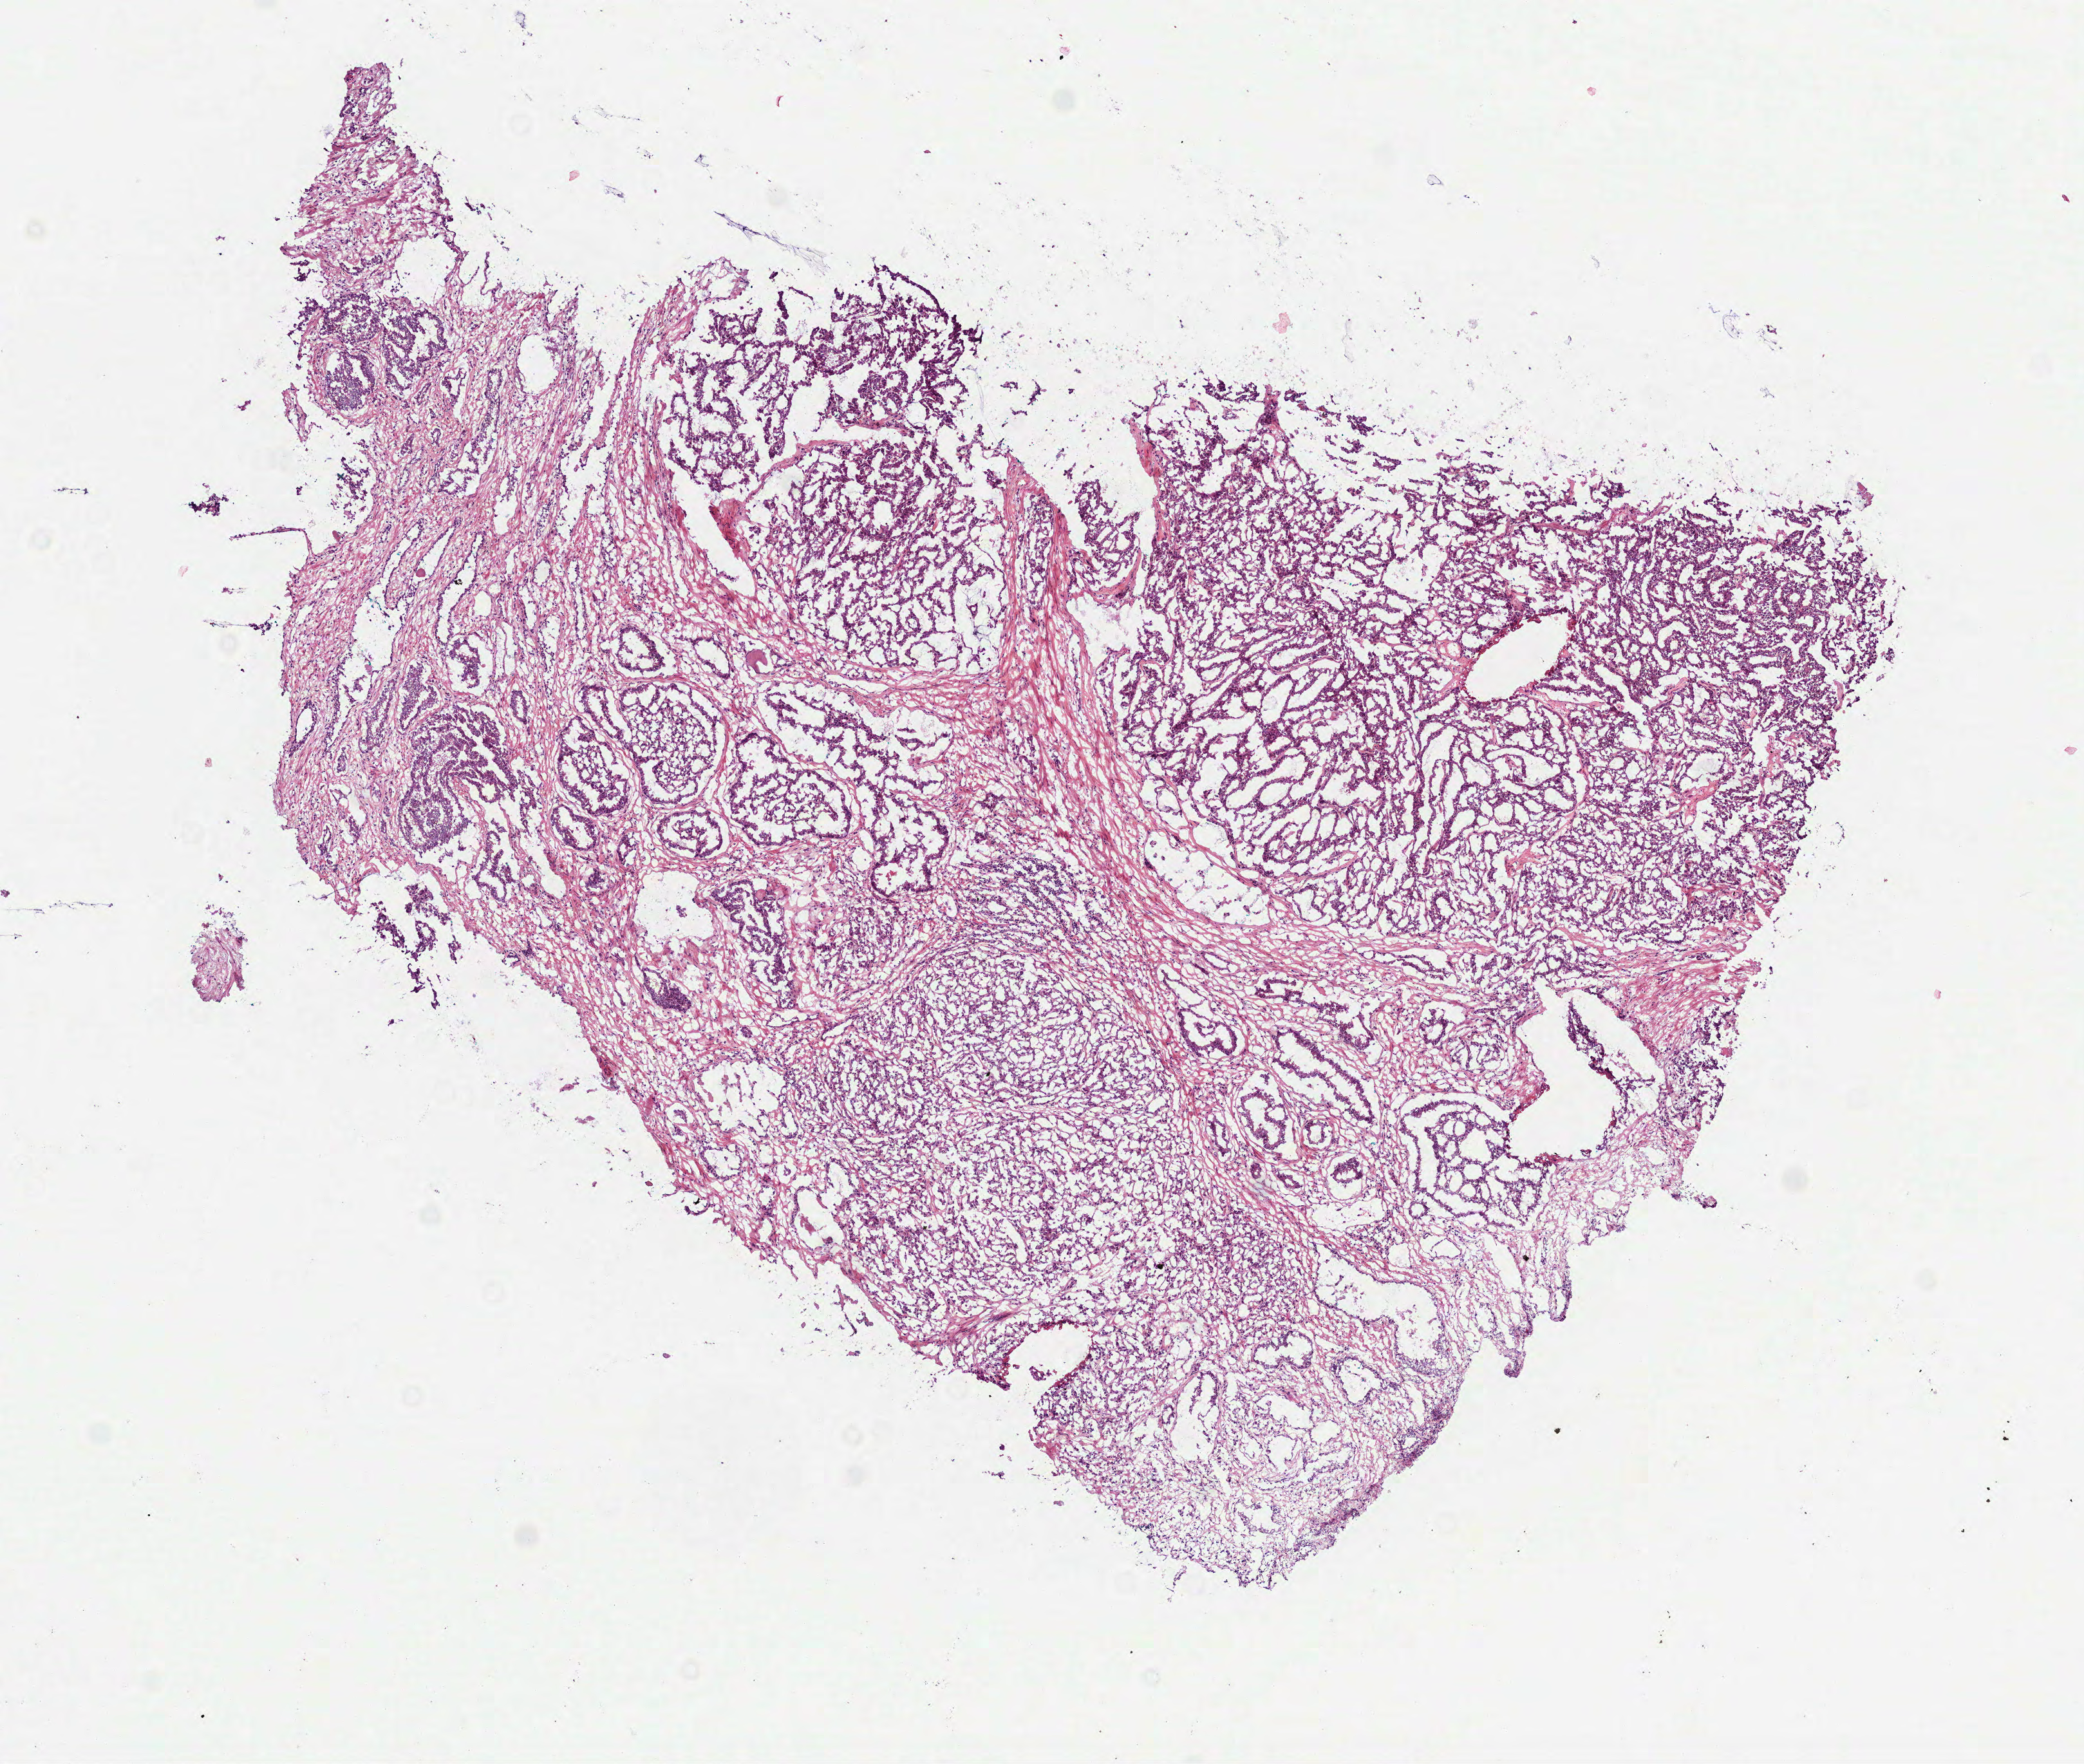
Whole-slide histology image, H&E-stained, shown as a low-resolution overview of the whole scanned area (about 6.5 x 5.5 mm), frozen section, prostate, primary tumour sample. Male, age 66 years at initial diagnosis. Gleason score: 7 (3+4). Slide review estimates, as recorded: tumour cells 70%, tumour nuclei 70%, normal cells 10%, stromal cells 20%, necrosis 0%.
Pathologic diagnosis: Acinar cell carcinoma (prostate gland). Lymph nodes positive (case pathology): 0 of 2 examined.